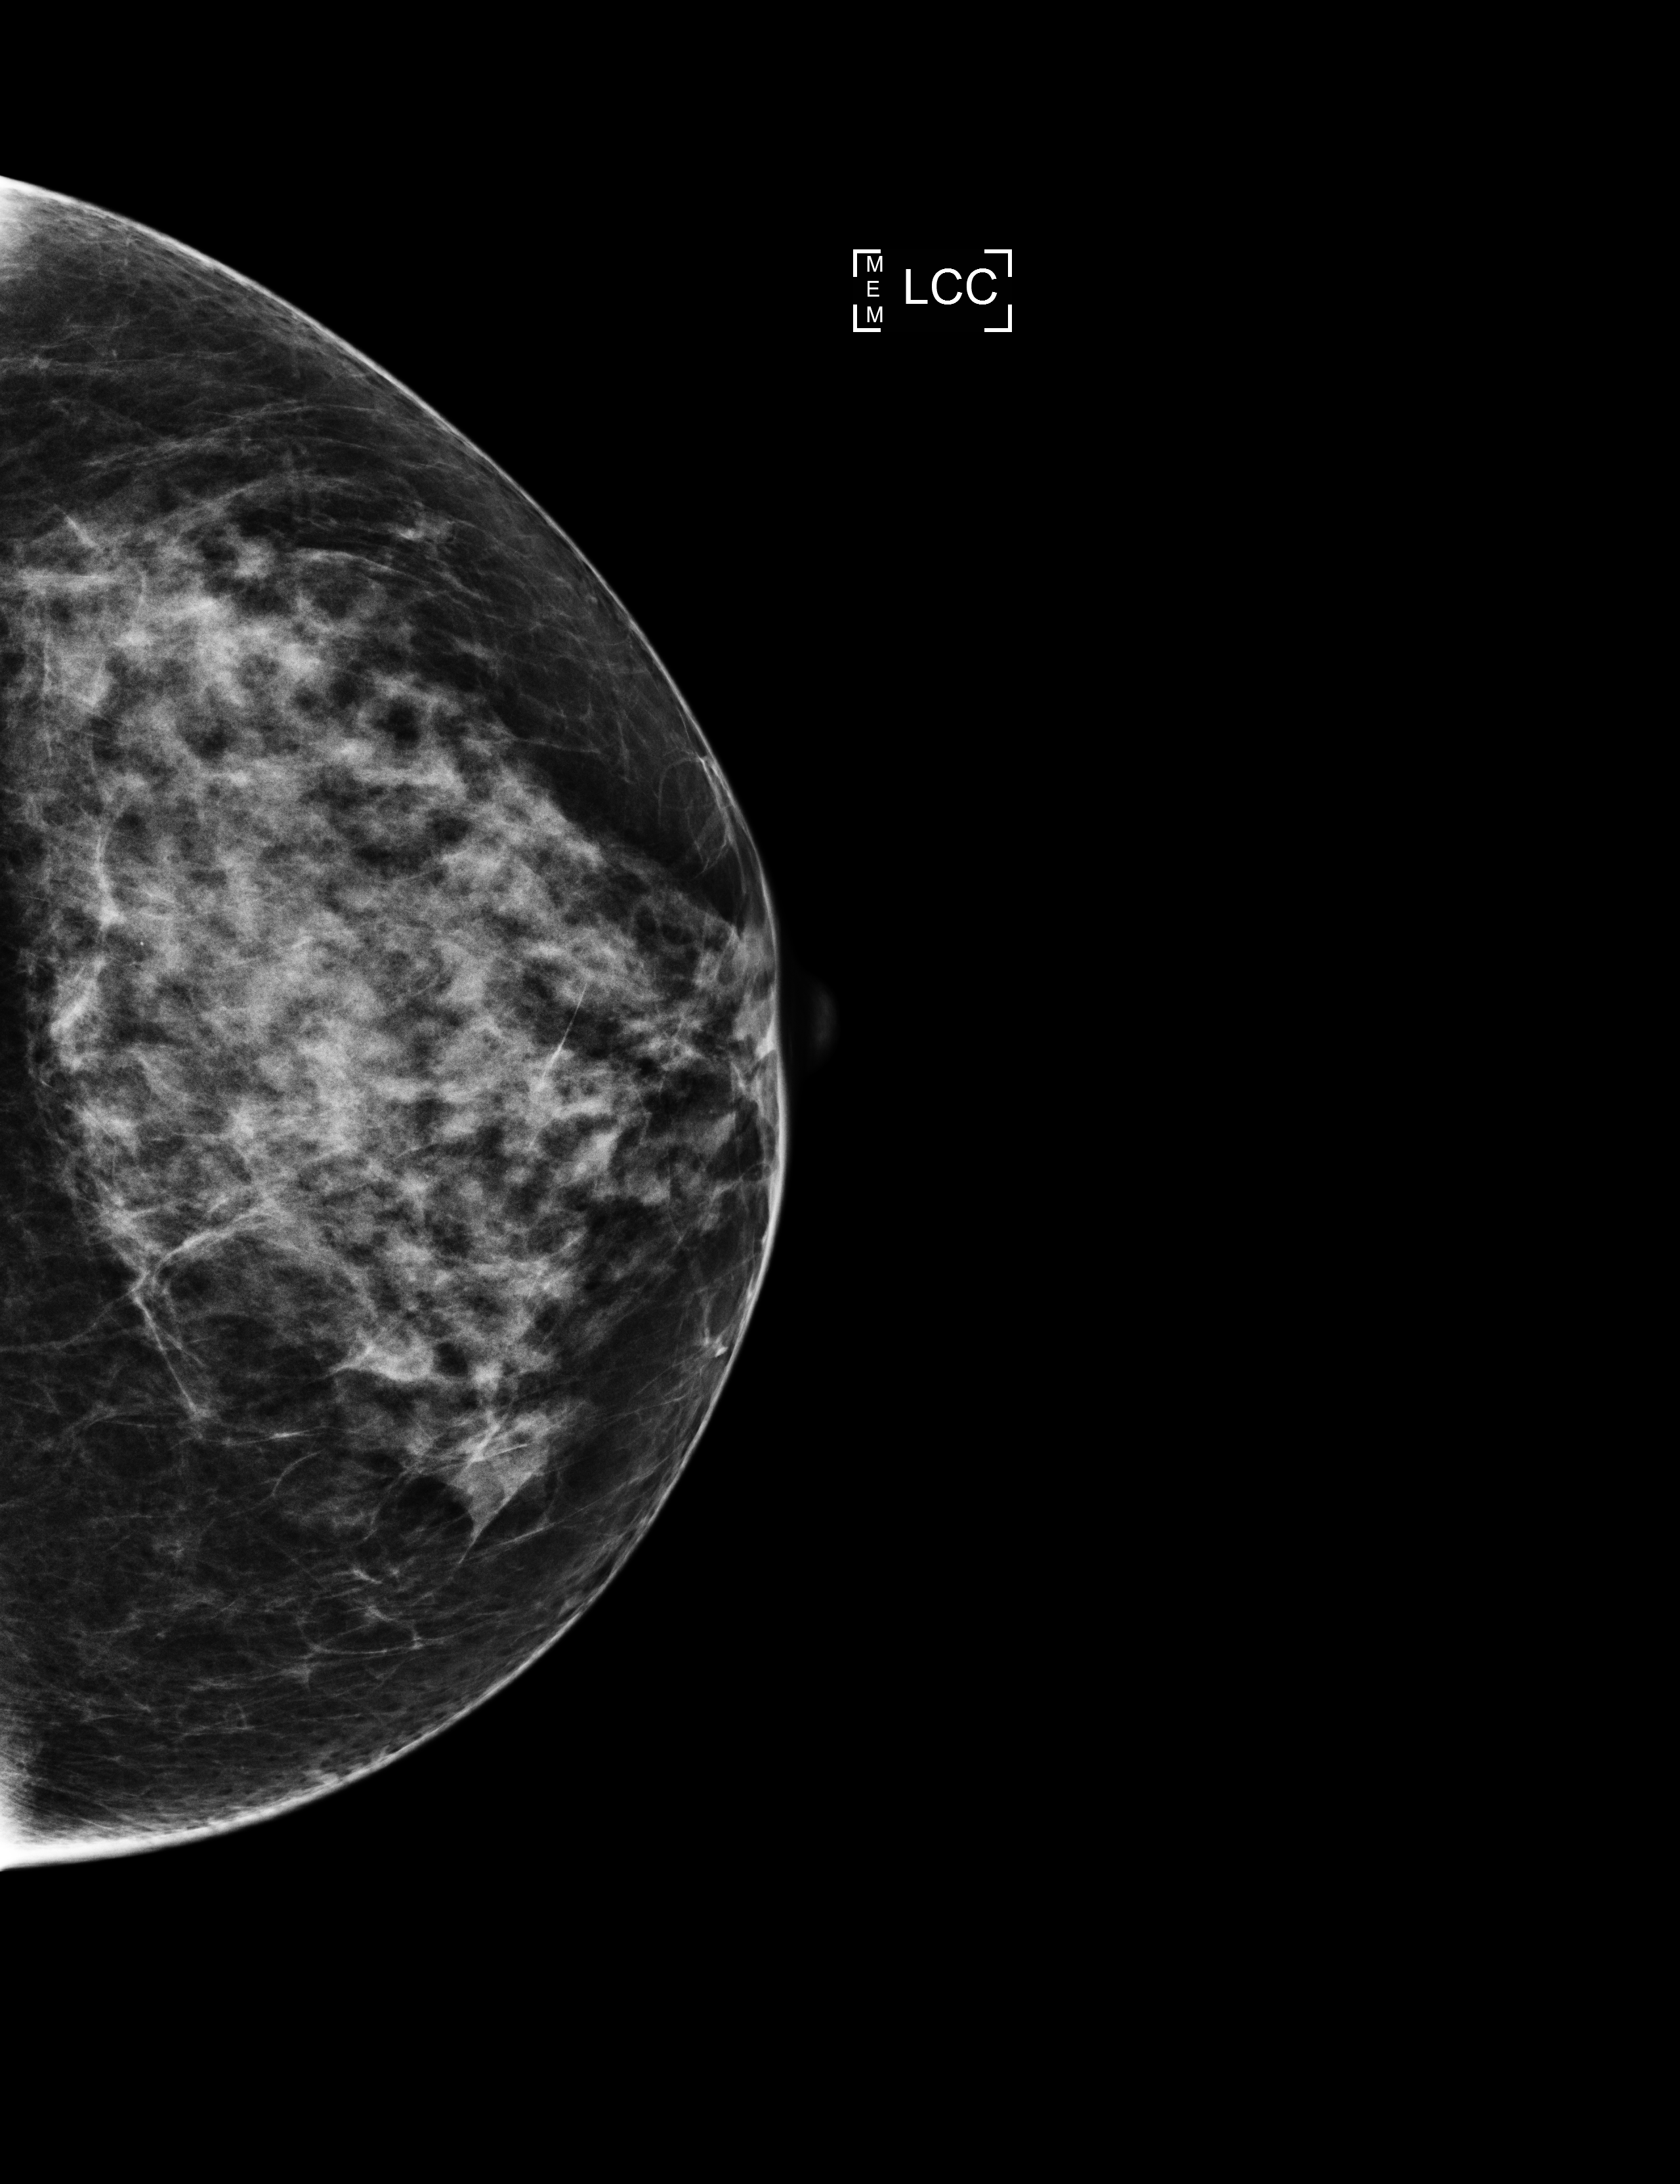
Annual screening mammography examination, compressed breast thickness 53 mm, system: Selenia Dimensions. Patient: female, 57 years.
Image type: full-field digital mammogram. Breast: left. Projection: CC view. Breast density at the screening exam (both breasts): heterogeneously dense (BI-RADS density category c). Final BI-RADS assessment for this screening round (tomosynthesis exam, both breasts): category 1. Recall: no recall after this screen.